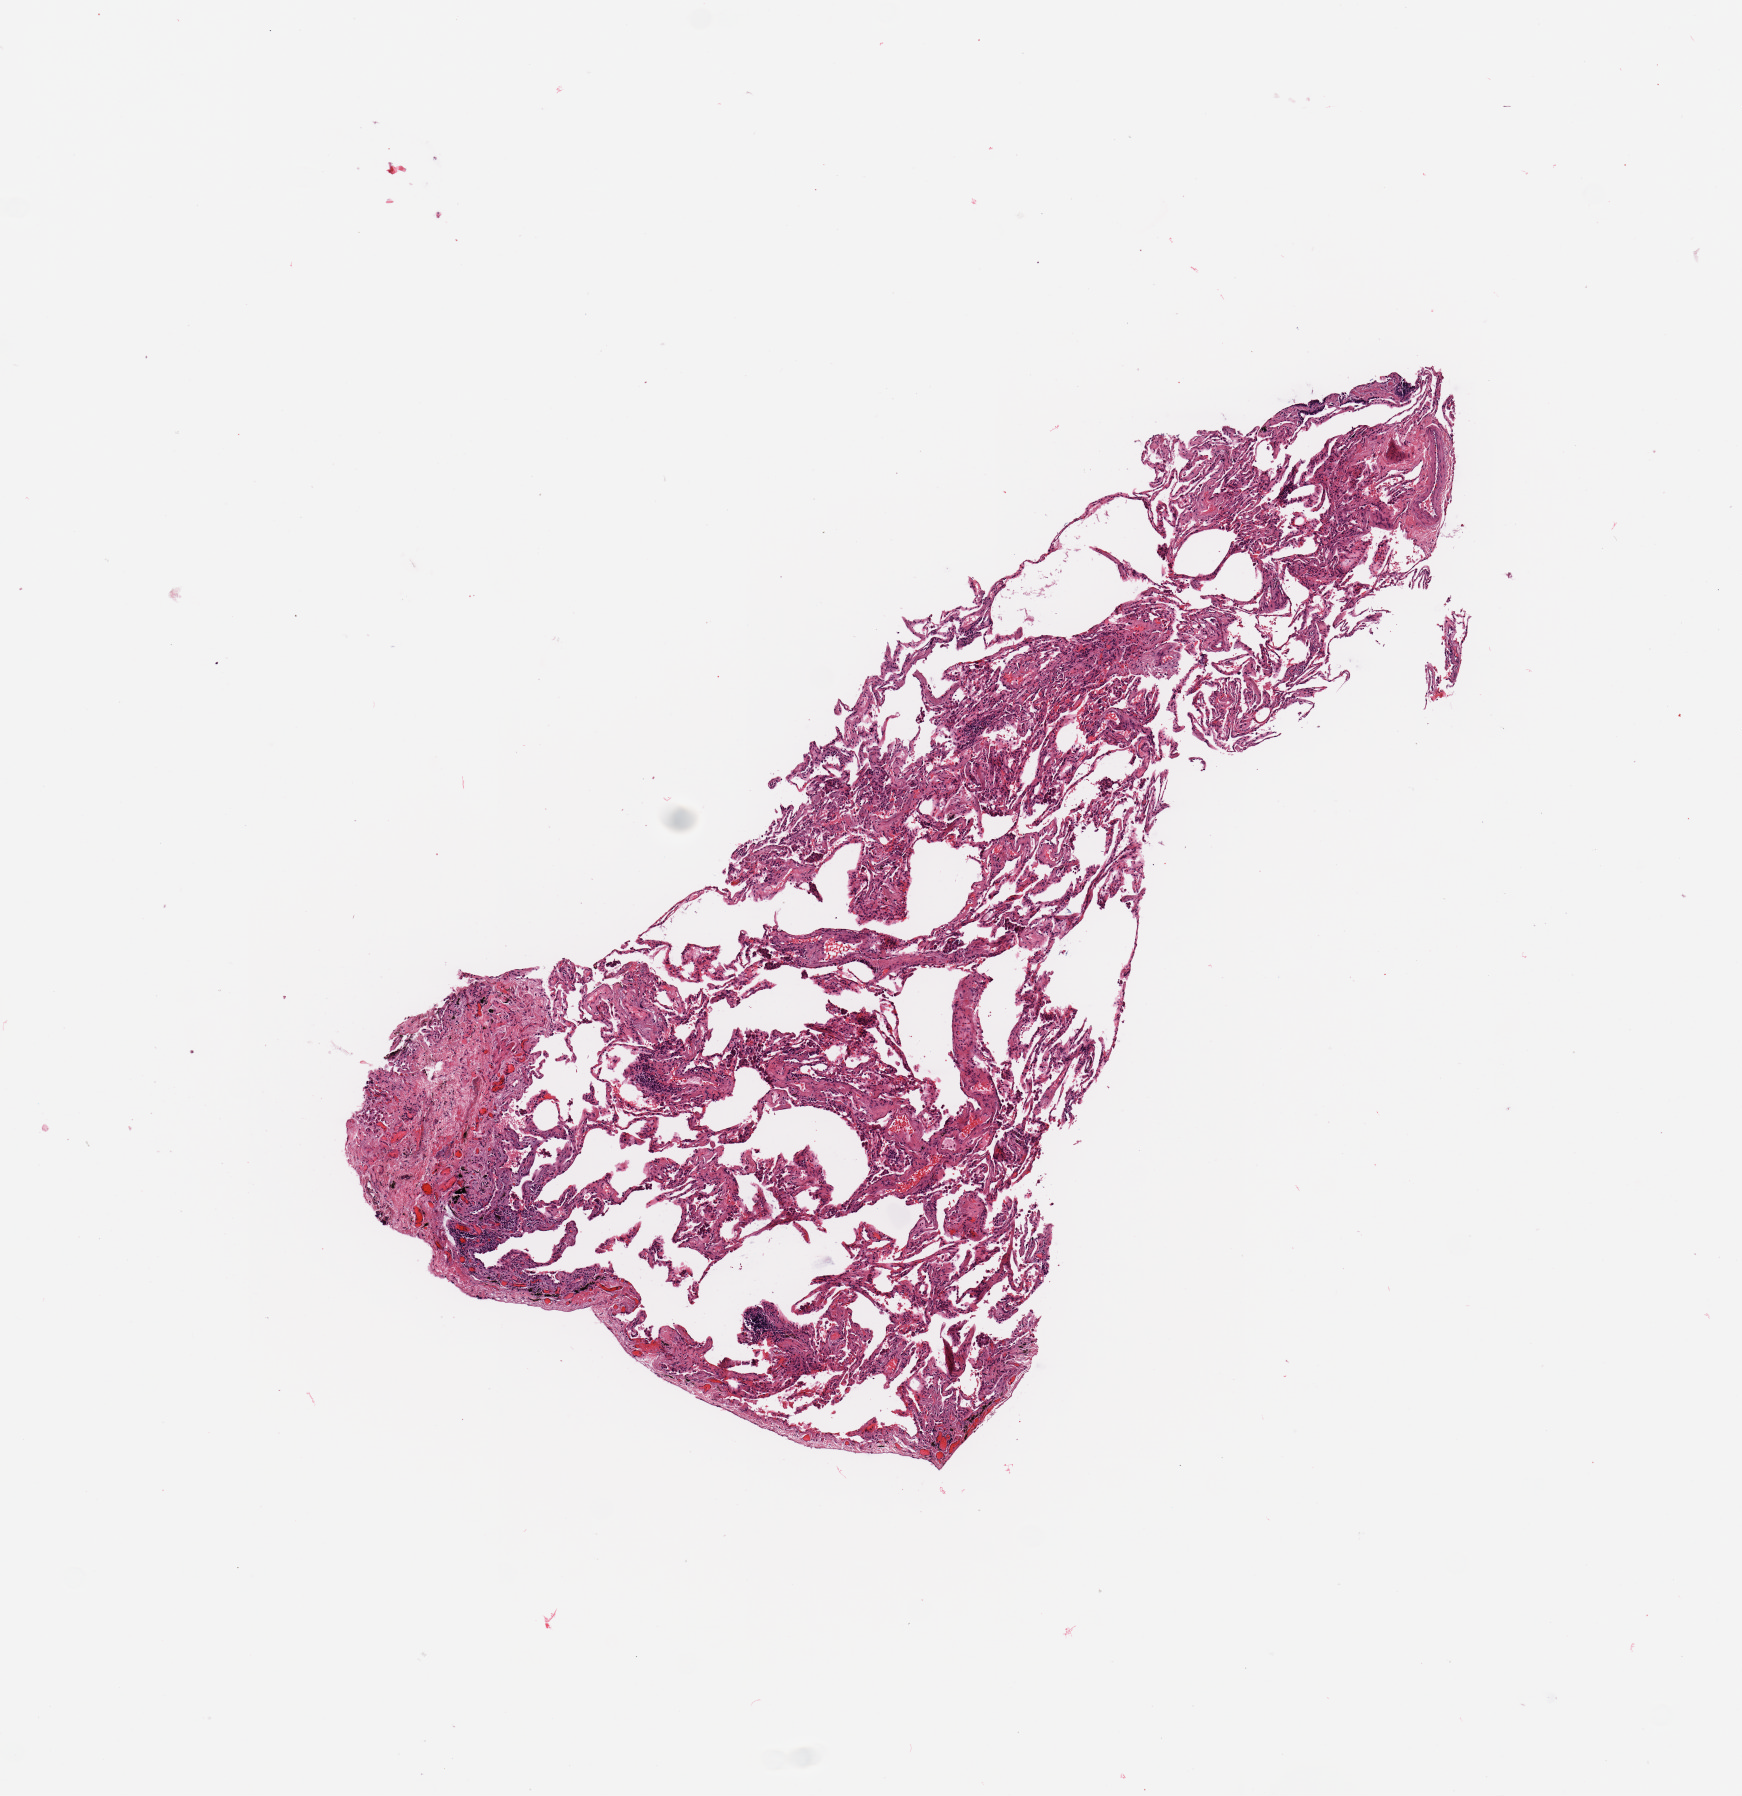
Digitized H&E tissue section (whole slide) — low-resolution overview of the scanned area, about 6.9 x 7.1 mm (from a 20x scan). Normal (non-tumour) tissue sample, sampled site: lung. Female, 67 y/o.
This section: normal (non-tumour) tissue from the same patient. Patient diagnosis: Adenocarcinoma, NOS.